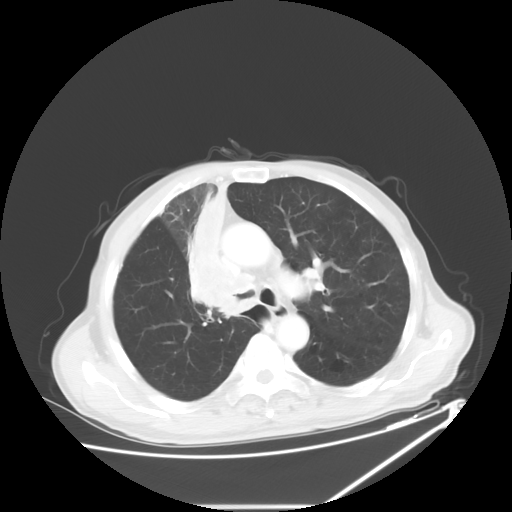
Chest CT, one axial slice. Position 41 of 60 along the scan axis. 120 kVp. Lung window (W 1500 / L -600 HU). 5 mm slice thickness. 512 × 512 image matrix, field of view 410 × 410 mm. Male patient, age 73 years. From the clinical record (not read from this slice): clinical TNM (as recorded): T2a N1 M0.
Structures marked on this image (rectangle marked by the reading radiologist):
- lung tumour (recorded histology: squamous cell carcinoma): bounding box (x1, y1, x2, y2) in pixels: (189, 188, 248, 319)